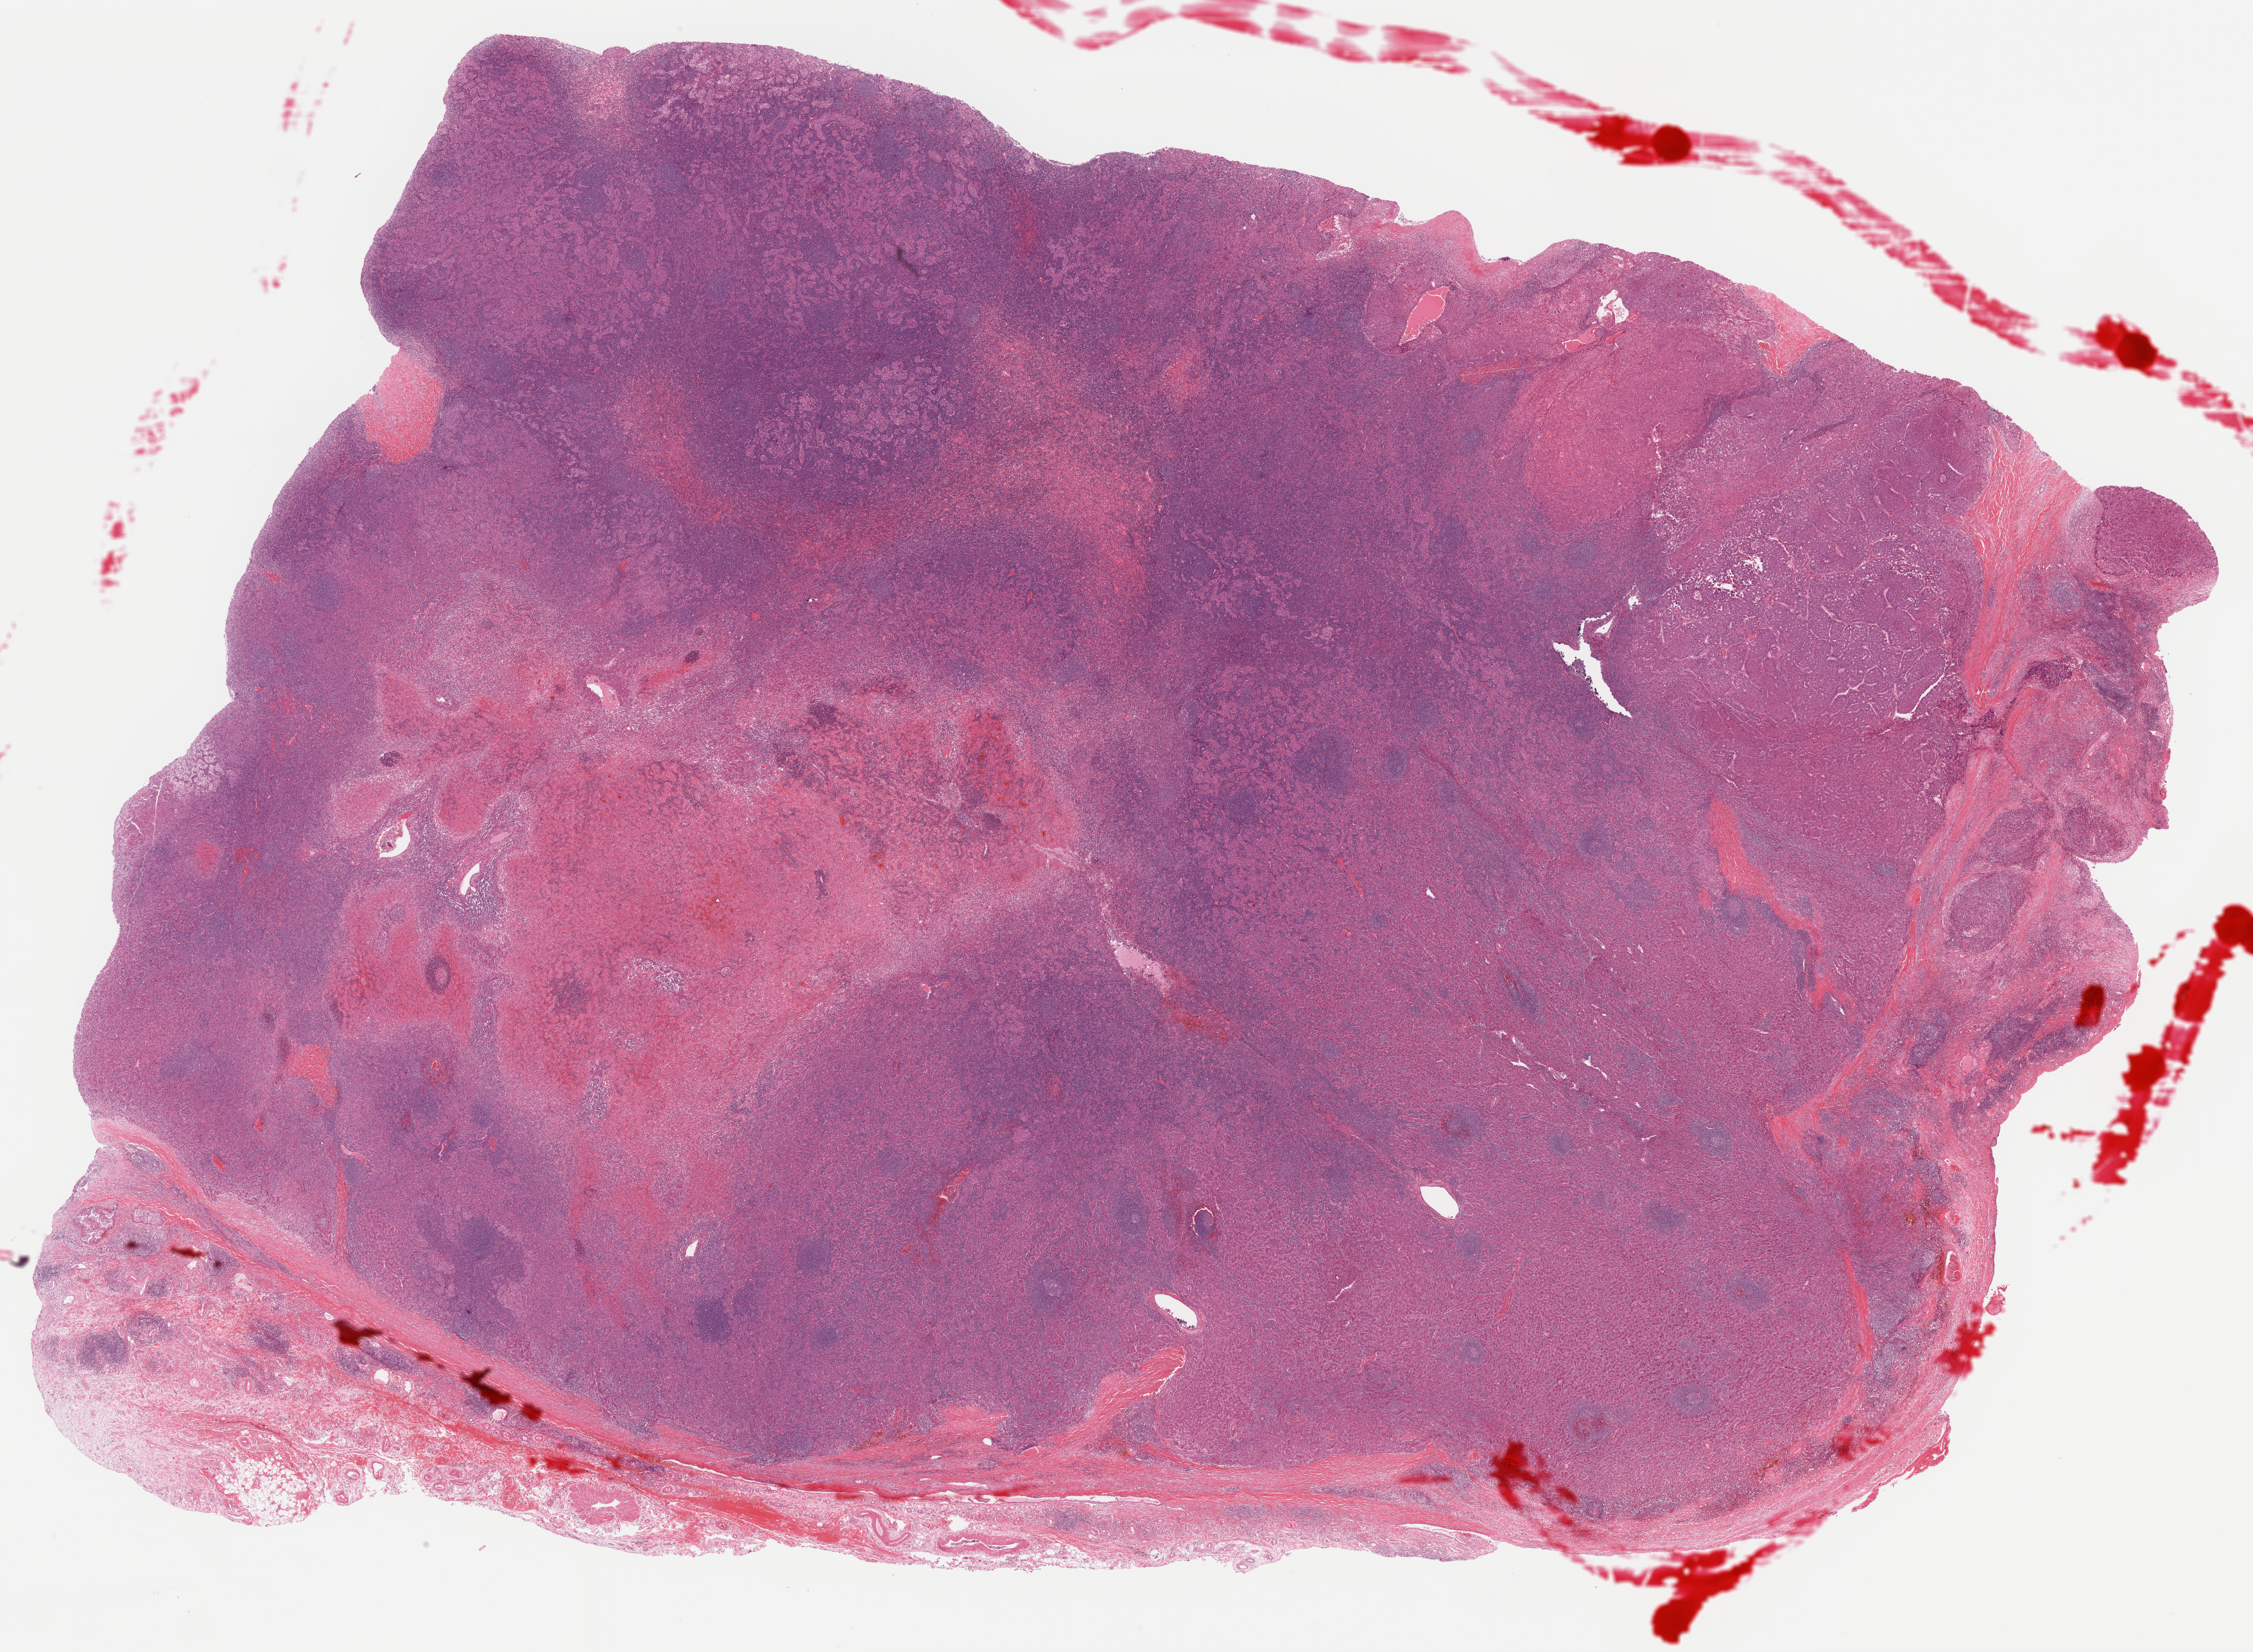
Hematoxylin and eosin (H&E) stained whole-slide image, low-resolution overview of the scanned area, about 27.7 x 20.3 mm (slide scanned at 40x). Formalin-fixed paraffin-embedded (FFPE) diagnostic section. Liver, primary tumour sample. Patient: female, age at initial diagnosis 60 years. Histologic grade: G2 (moderately differentiated).
AJCC pathologic stage: II. Diagnosis: Hepatocellular carcinoma, NOS.